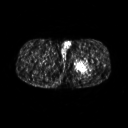
FDG PET of an extremity soft-tissue mass (from a PET/CT study), one axial slice. 3.27 mm slice thickness. 128 × 128 image matrix. Male patient, age 27 years. Case-level facts recorded for this patient, not image findings: histological type: extraskeletal osteosarcoma; grade: high; site of the primary tumour: left adductur.
Outlined on this slice (expert contour drawn on MRI and transferred to this co-registered scan by the dataset authors):
- gross tumour volume (mass): bounding box <72,55,95,75> (left, top, right, bottom; pixels)